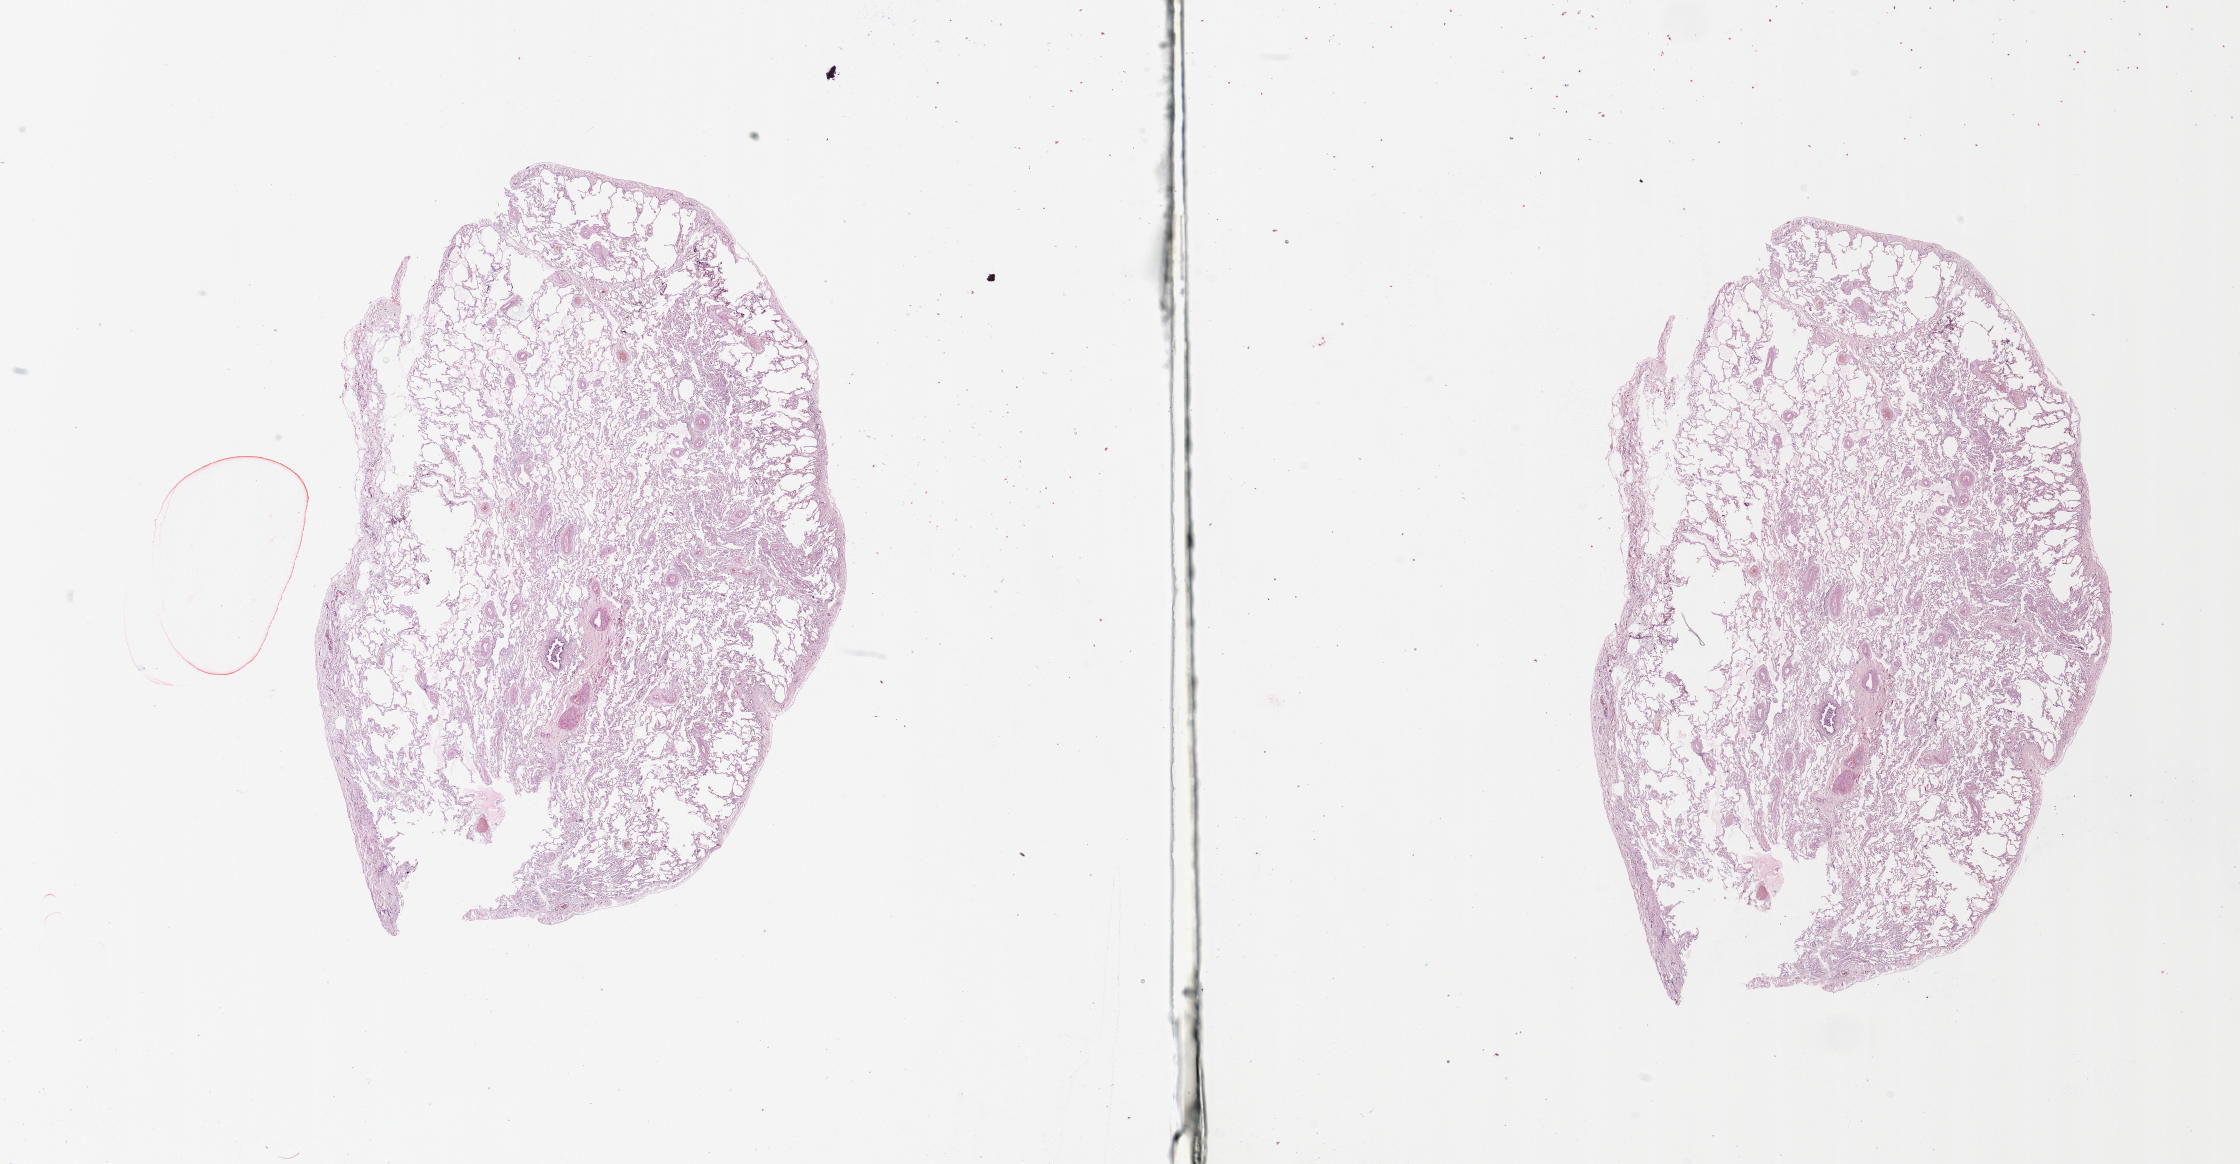
H&E-stained whole-slide image — shown as a low-resolution overview of the whole scanned area (about 35.4 x 18.4 mm, from a 20x scan); normal (non-tumour) tissue sample, sampled site: lung. Patient: male, age 68 years.
This section: normal (non-tumour) tissue from the same patient. Patient diagnosis: Adenocarcinoma, NOS.